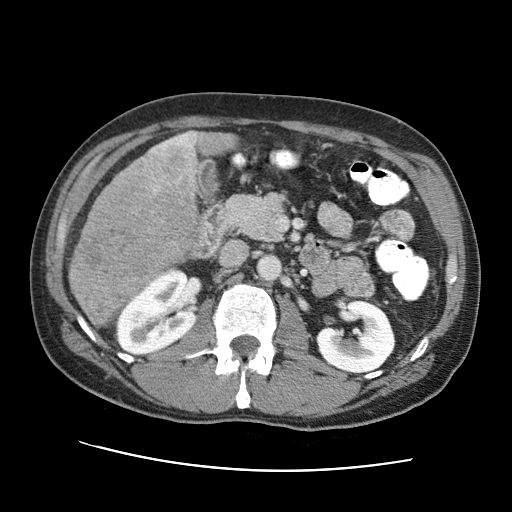
Contrast-enhanced abdominal CT (liver protocol), one axial slice. Slice 28 of 95 in the series (ordered by position). 120 kVp. One of 2 acquisitions stored at this slice position. Soft-tissue window (W 400 / L 40 HU). 512 × 512 image matrix, field of view 360 × 360 mm. From the clinical record (not read from this slice): diagnosis: hepatocellular carcinoma (patient treated with transarterial chemoembolisation; whether this scan precedes or follows treatment is not stated here); TNM stage (as recorded): Stage-IVA; Child-Pugh class: A; tumour differentiation: moderately differentiated.
Outlined on this slice (semi-automatic segmentation, software-assisted and operator-edited):
- liver parenchyma outside the tumour (the mass and vessels are separate outlines, so this box may not span the whole liver): bounding box [x1, y1, x2, y2] px = [68, 132, 235, 296]
- mass: [68, 131, 197, 329]